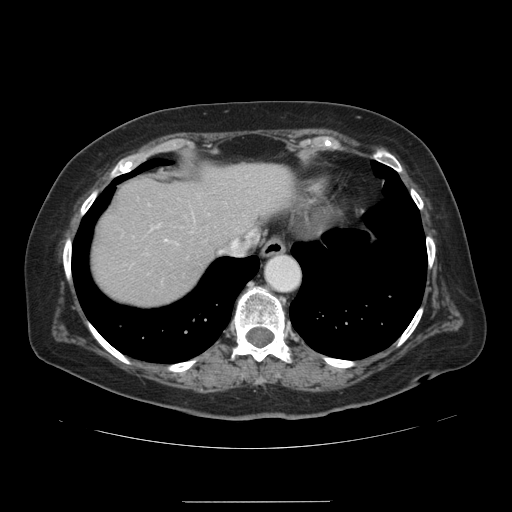
Contrast-enhanced abdominal CT, one axial slice. Position 116 of 141 along the scan axis. Soft-tissue window (W 400 / L 40 HU). 2.5 mm slice thickness. 512 × 512 image matrix. Female patient, age 74 years. From the clinical record (not read from this slice): diagnosis: colorectal cancer liver metastases, imaged before liver resection; multiple liver metastases: yes; largest metastasis: 7 cm.
Annotated regions visible in this slice (manually delineated by an expert):
- hepatic veins: box from (x=219, y=236) to (x=252, y=254) px
- liver: (x=94, y=163)–(x=292, y=307)
- planned liver remnant (the part of the liver to remain after resection): (x=94, y=163)–(x=292, y=307)
- portal vein (with intrahepatic branches): (x=164, y=231)–(x=253, y=241)